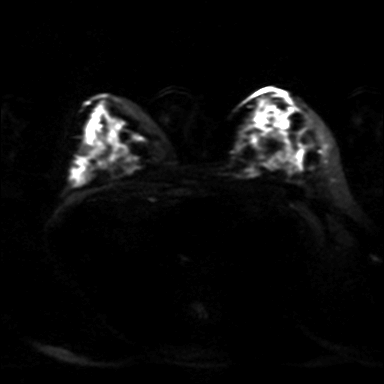
Breast MRI, one axial slice; position 22 of 36 along the scan axis; diffusion-weighted series; image 2 of 4 stored at this slice position (different b-values; order by instance number); 3 T; 384 × 384 image matrix, field of view 320 × 320 mm. Female patient.
Annotated regions visible in this slice (manually delineated by an expert):
- tumour on diffusion-weighted imaging: bounding box (x1, y1, x2, y2) in pixels: (271, 113, 290, 127)